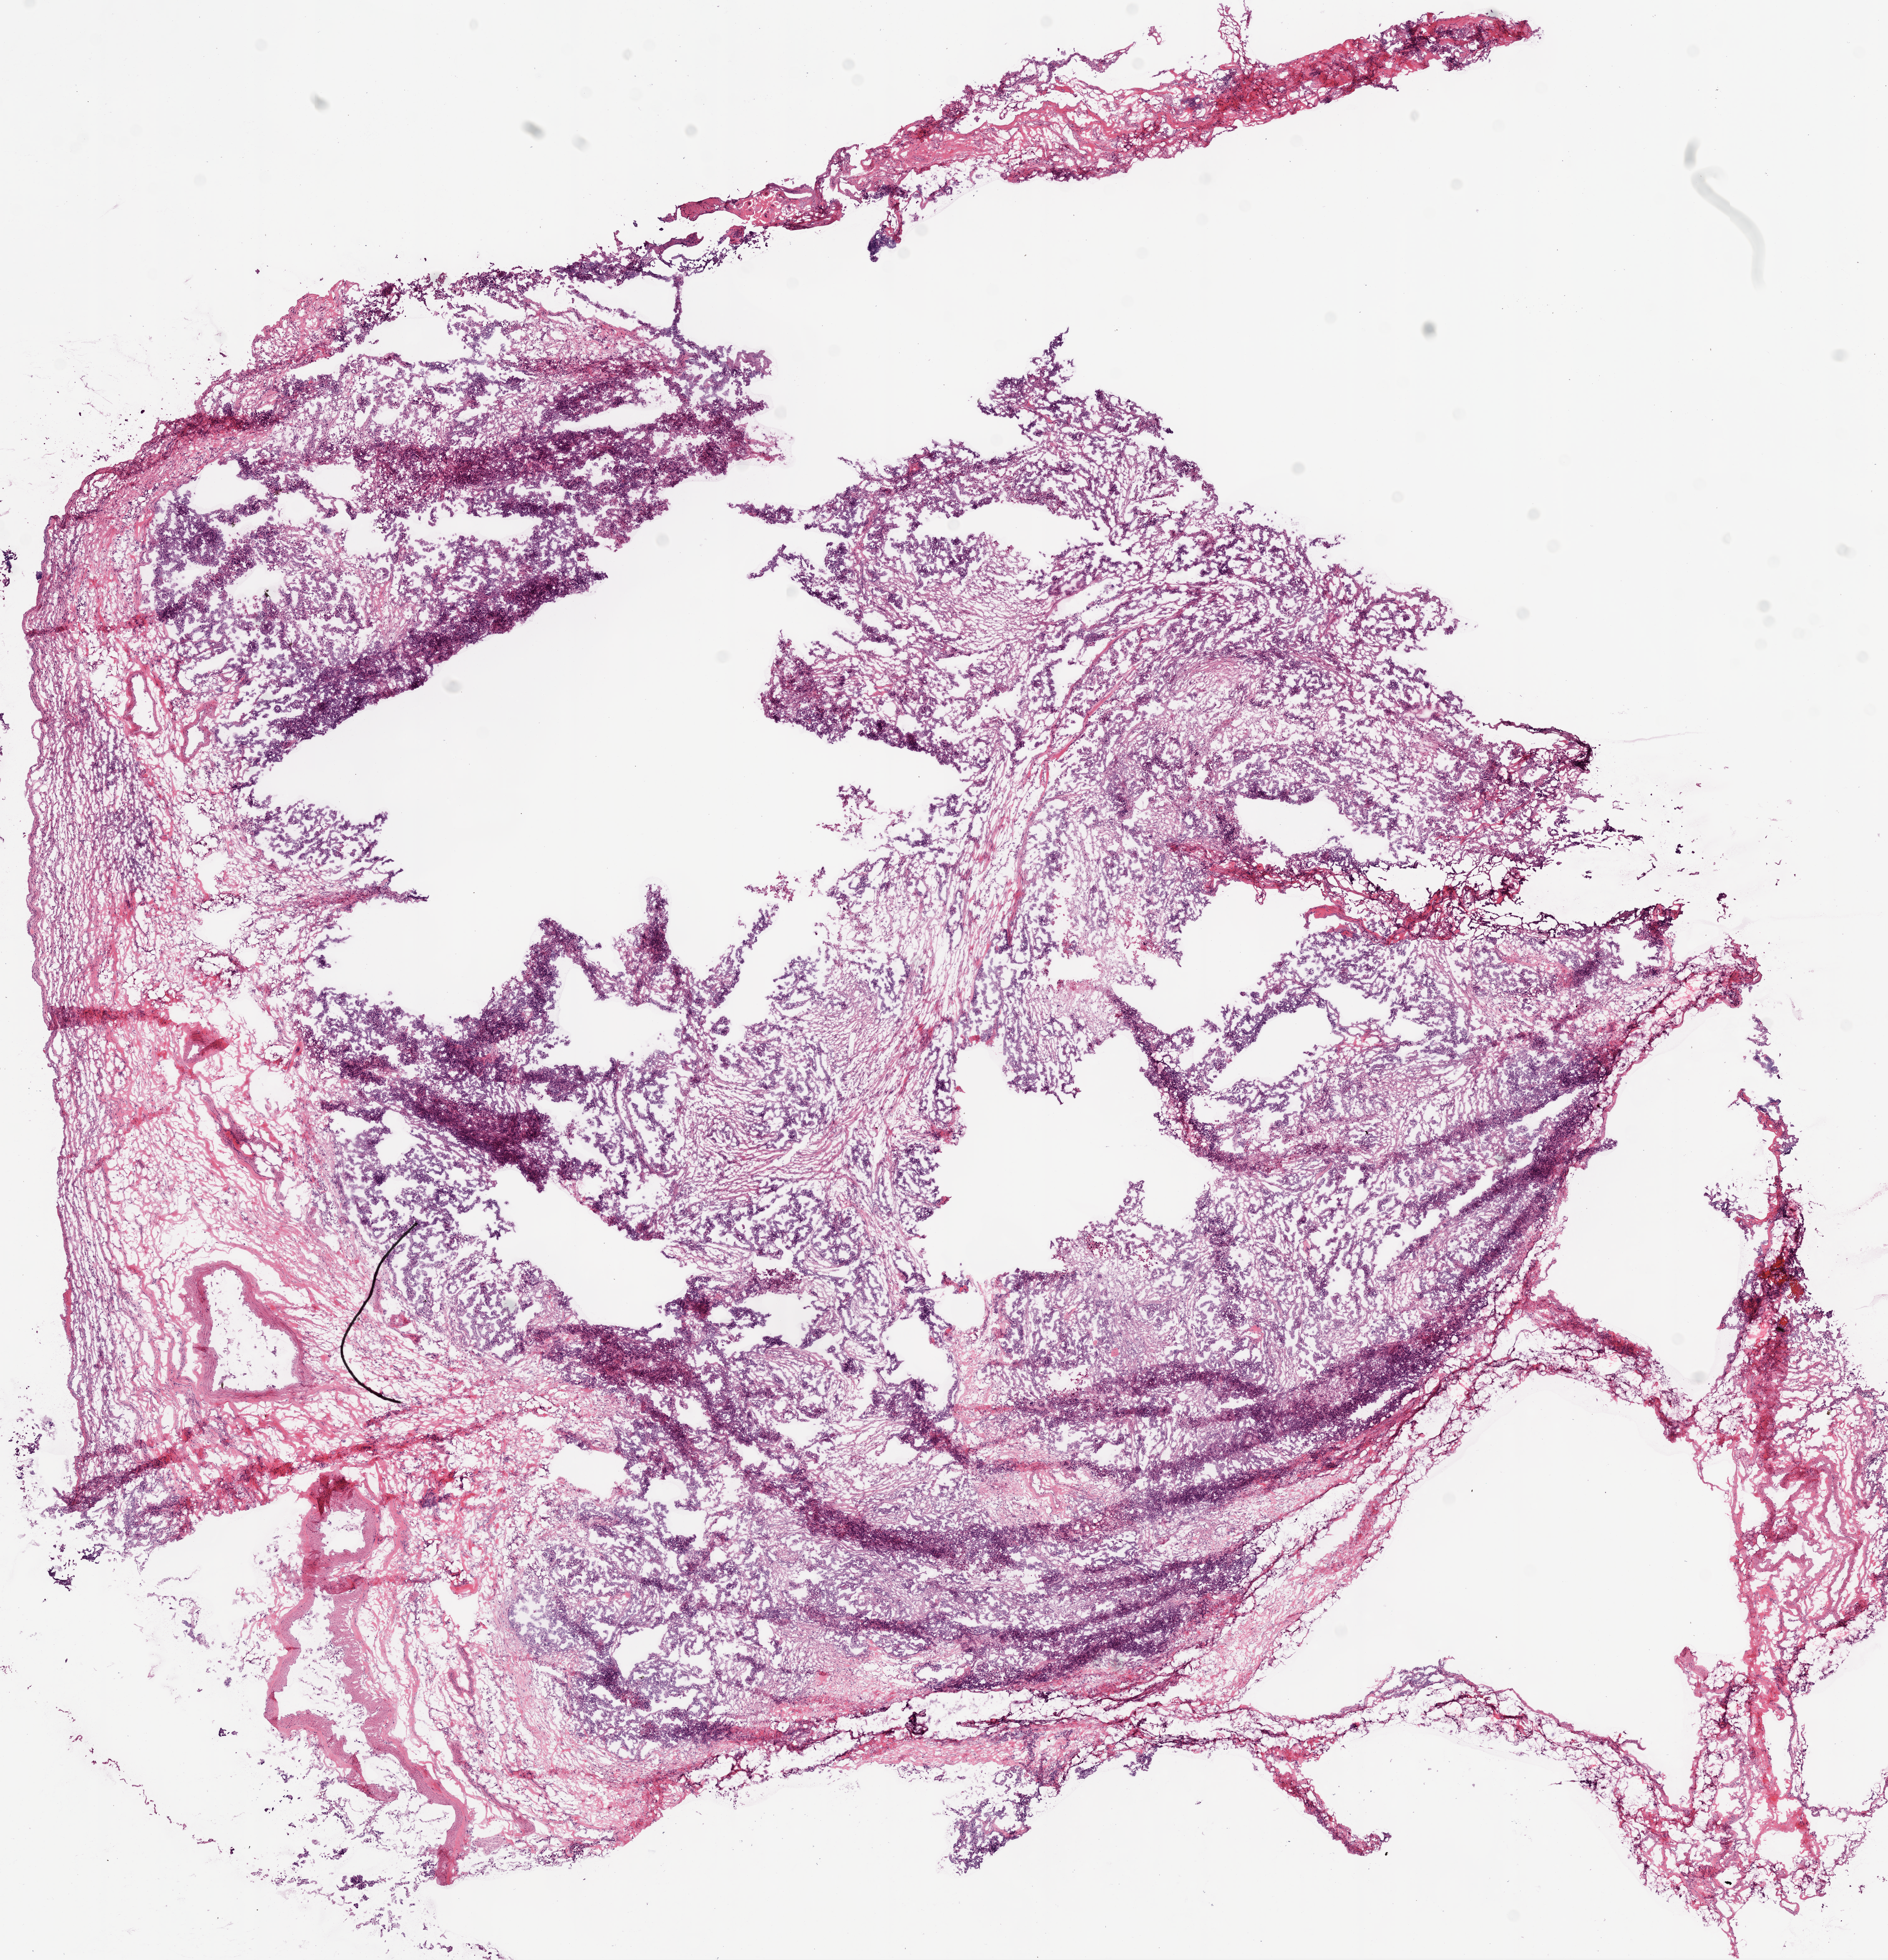
Hematoxylin and eosin (H&E) stained whole-slide image, shown as a low-resolution overview of the whole scanned area (about 12.0 x 12.5 mm), frozen section, sample: primary tumour, ovary. Female, age 76 years at initial diagnosis. Histologic grade: G2 (moderately differentiated). Composition of this section per pathologist review: tumour cells 60%, tumour nuclei 70%, normal cells 0%, stromal cells 40%, necrosis 0%. Inflammatory infiltration, as recorded: lymphocyte infiltration 60%, monocyte infiltration 10%, neutrophil infiltration 30%.
• laterality: right
• FIGO stage: IIIC
• diagnosis: Serous cystadenocarcinoma, NOS